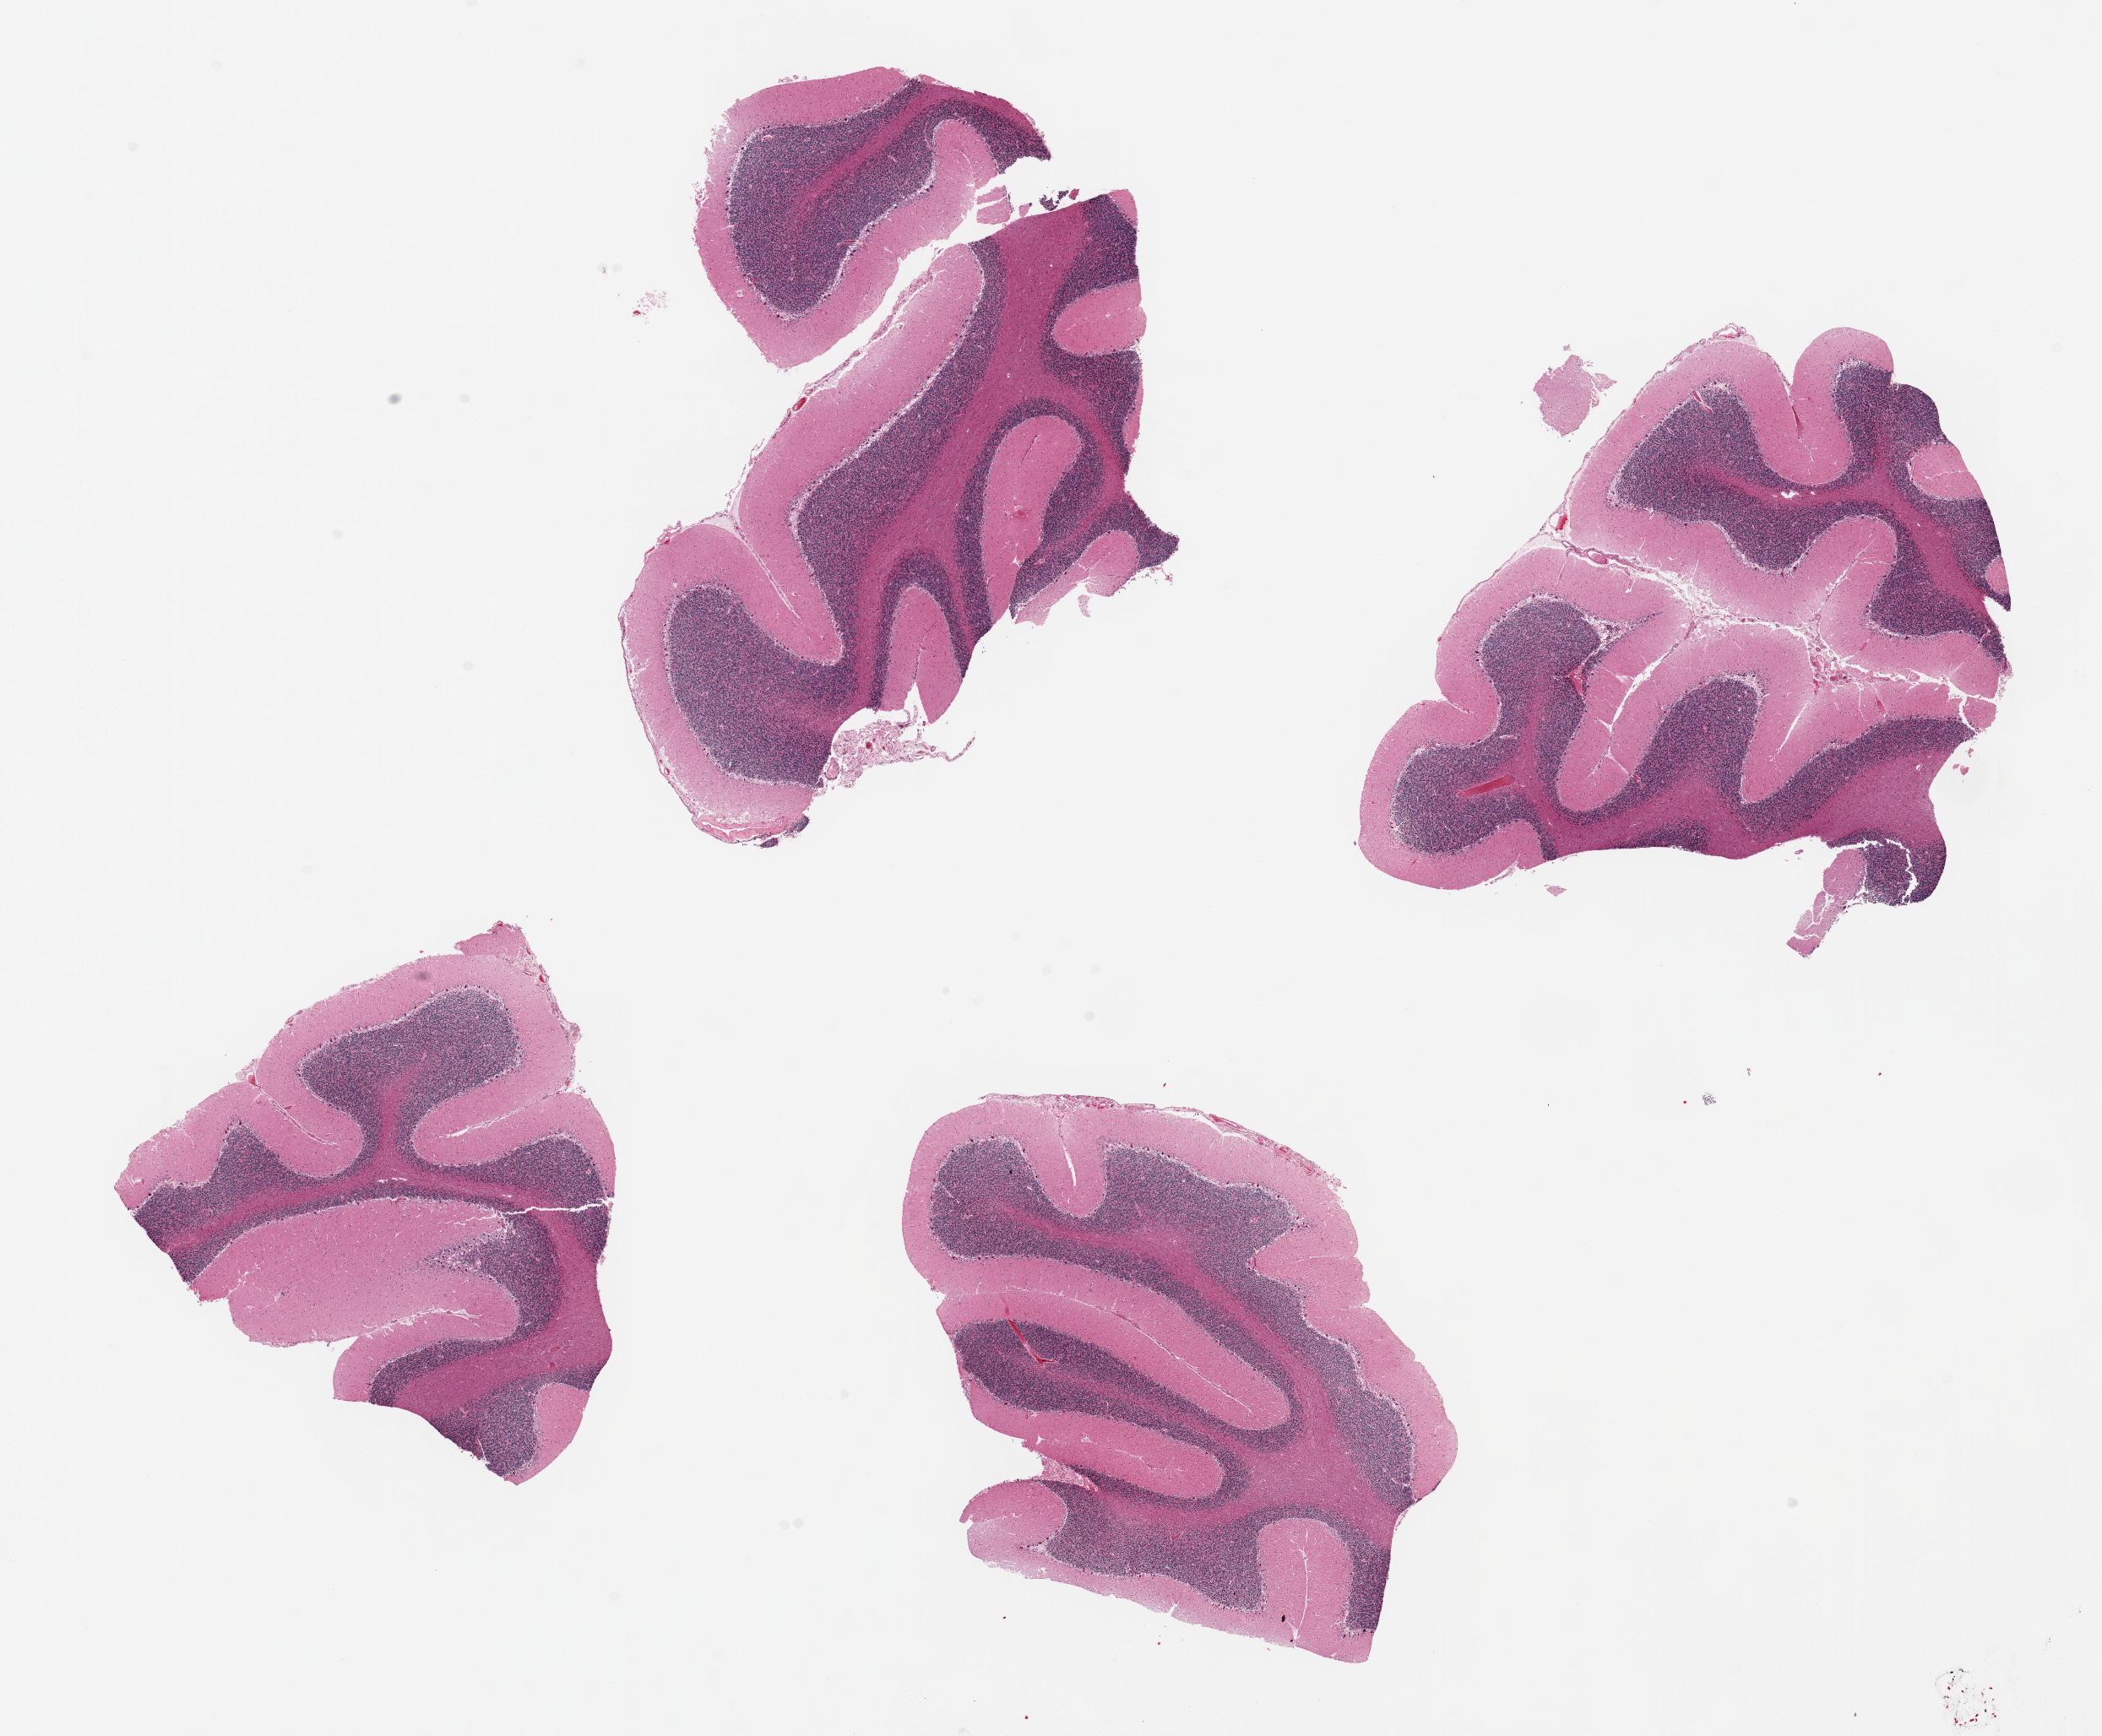
Digitized hematoxylin and eosin (H&E)-stained section, brightfield, whole scanned area (about 19.7 x 16.3 mm) shown as a low-resolution overview; PAXgene-fixed, paraffin-embedded tissue; target tissue: cerebellum; donor tissue sample. Donor: female.
Reviewer comment on this tissue sample: 4 ~5x5mm aliquots.